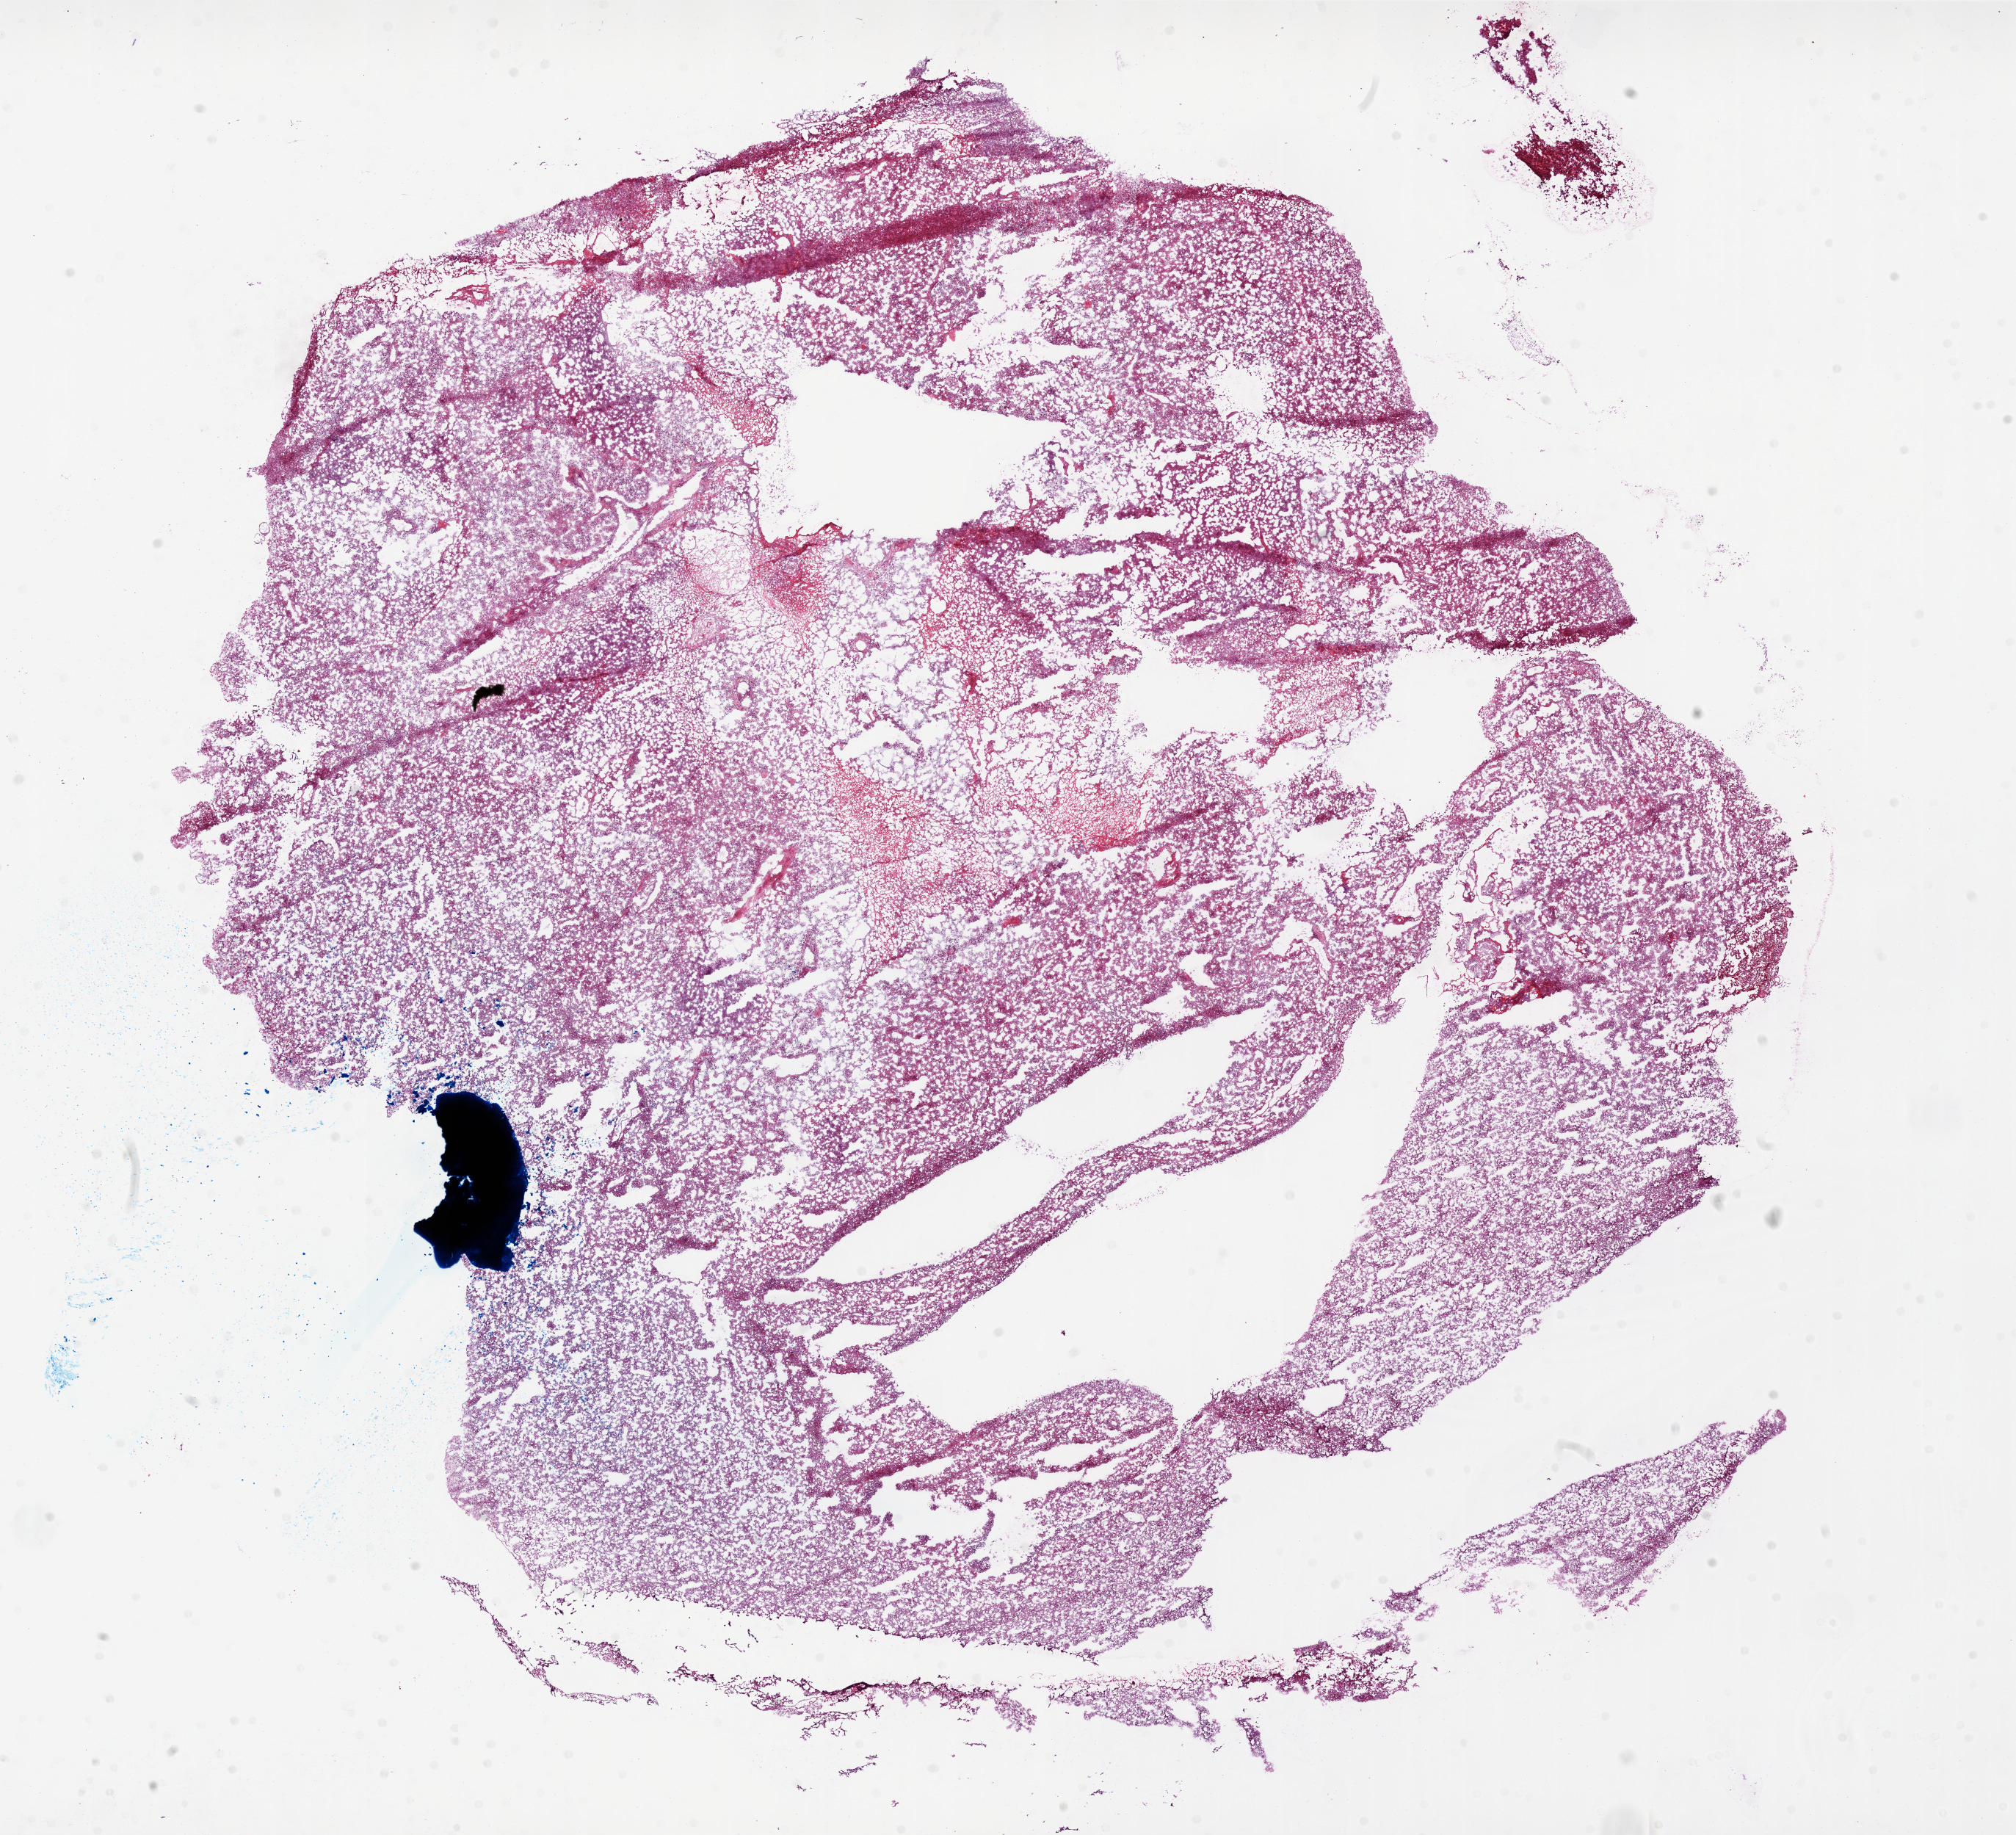
Digitized H&E tissue section (whole slide) — shown as a low-resolution overview of the whole scanned area (about 22.0 x 20.0 mm). Frozen section from the top of the tissue portion. Brain, primary tumour sample. Male patient; age at initial diagnosis 61 years. Pathologist review of this section (percent, as recorded): tumour cells 90%, tumour nuclei 100%, normal cells 0%, stromal cells 0%, necrosis 10%.
Diagnosis: Glioblastoma.